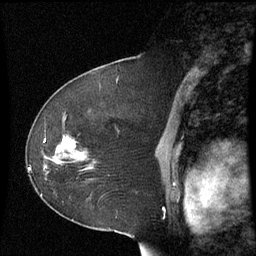
Breast MRI (dynamic contrast-enhanced), one sagittal slice; slice 37 of 60 in the series (ordered by position); dynamic contrast-enhanced series, image 2 of 3 at this slice position (ordered by acquisition); 1.5 T; TE 4.2 ms, TR 8.9 ms; 2.3 mm slice thickness; 256 × 256 image matrix, field of view 210 × 210 mm. Female patient, age 51 years. Case-level facts recorded for this patient, not image findings: setting: breast cancer imaged before/during neoadjuvant chemotherapy; receptor status: HR-positive, HER2-negative.
Outlined on this slice (semi-automatic segmentation, software-assisted and operator-edited):
- analysis volume of interest (the breast-tissue region the enhancement analysis was run in; not a lesion): bounding box <50,117,94,173> (left, top, right, bottom; pixels)
- tumour enhancement mask (voxels above the 70 % enhancement threshold inside the analysis volume of interest): <58,138,77,151>